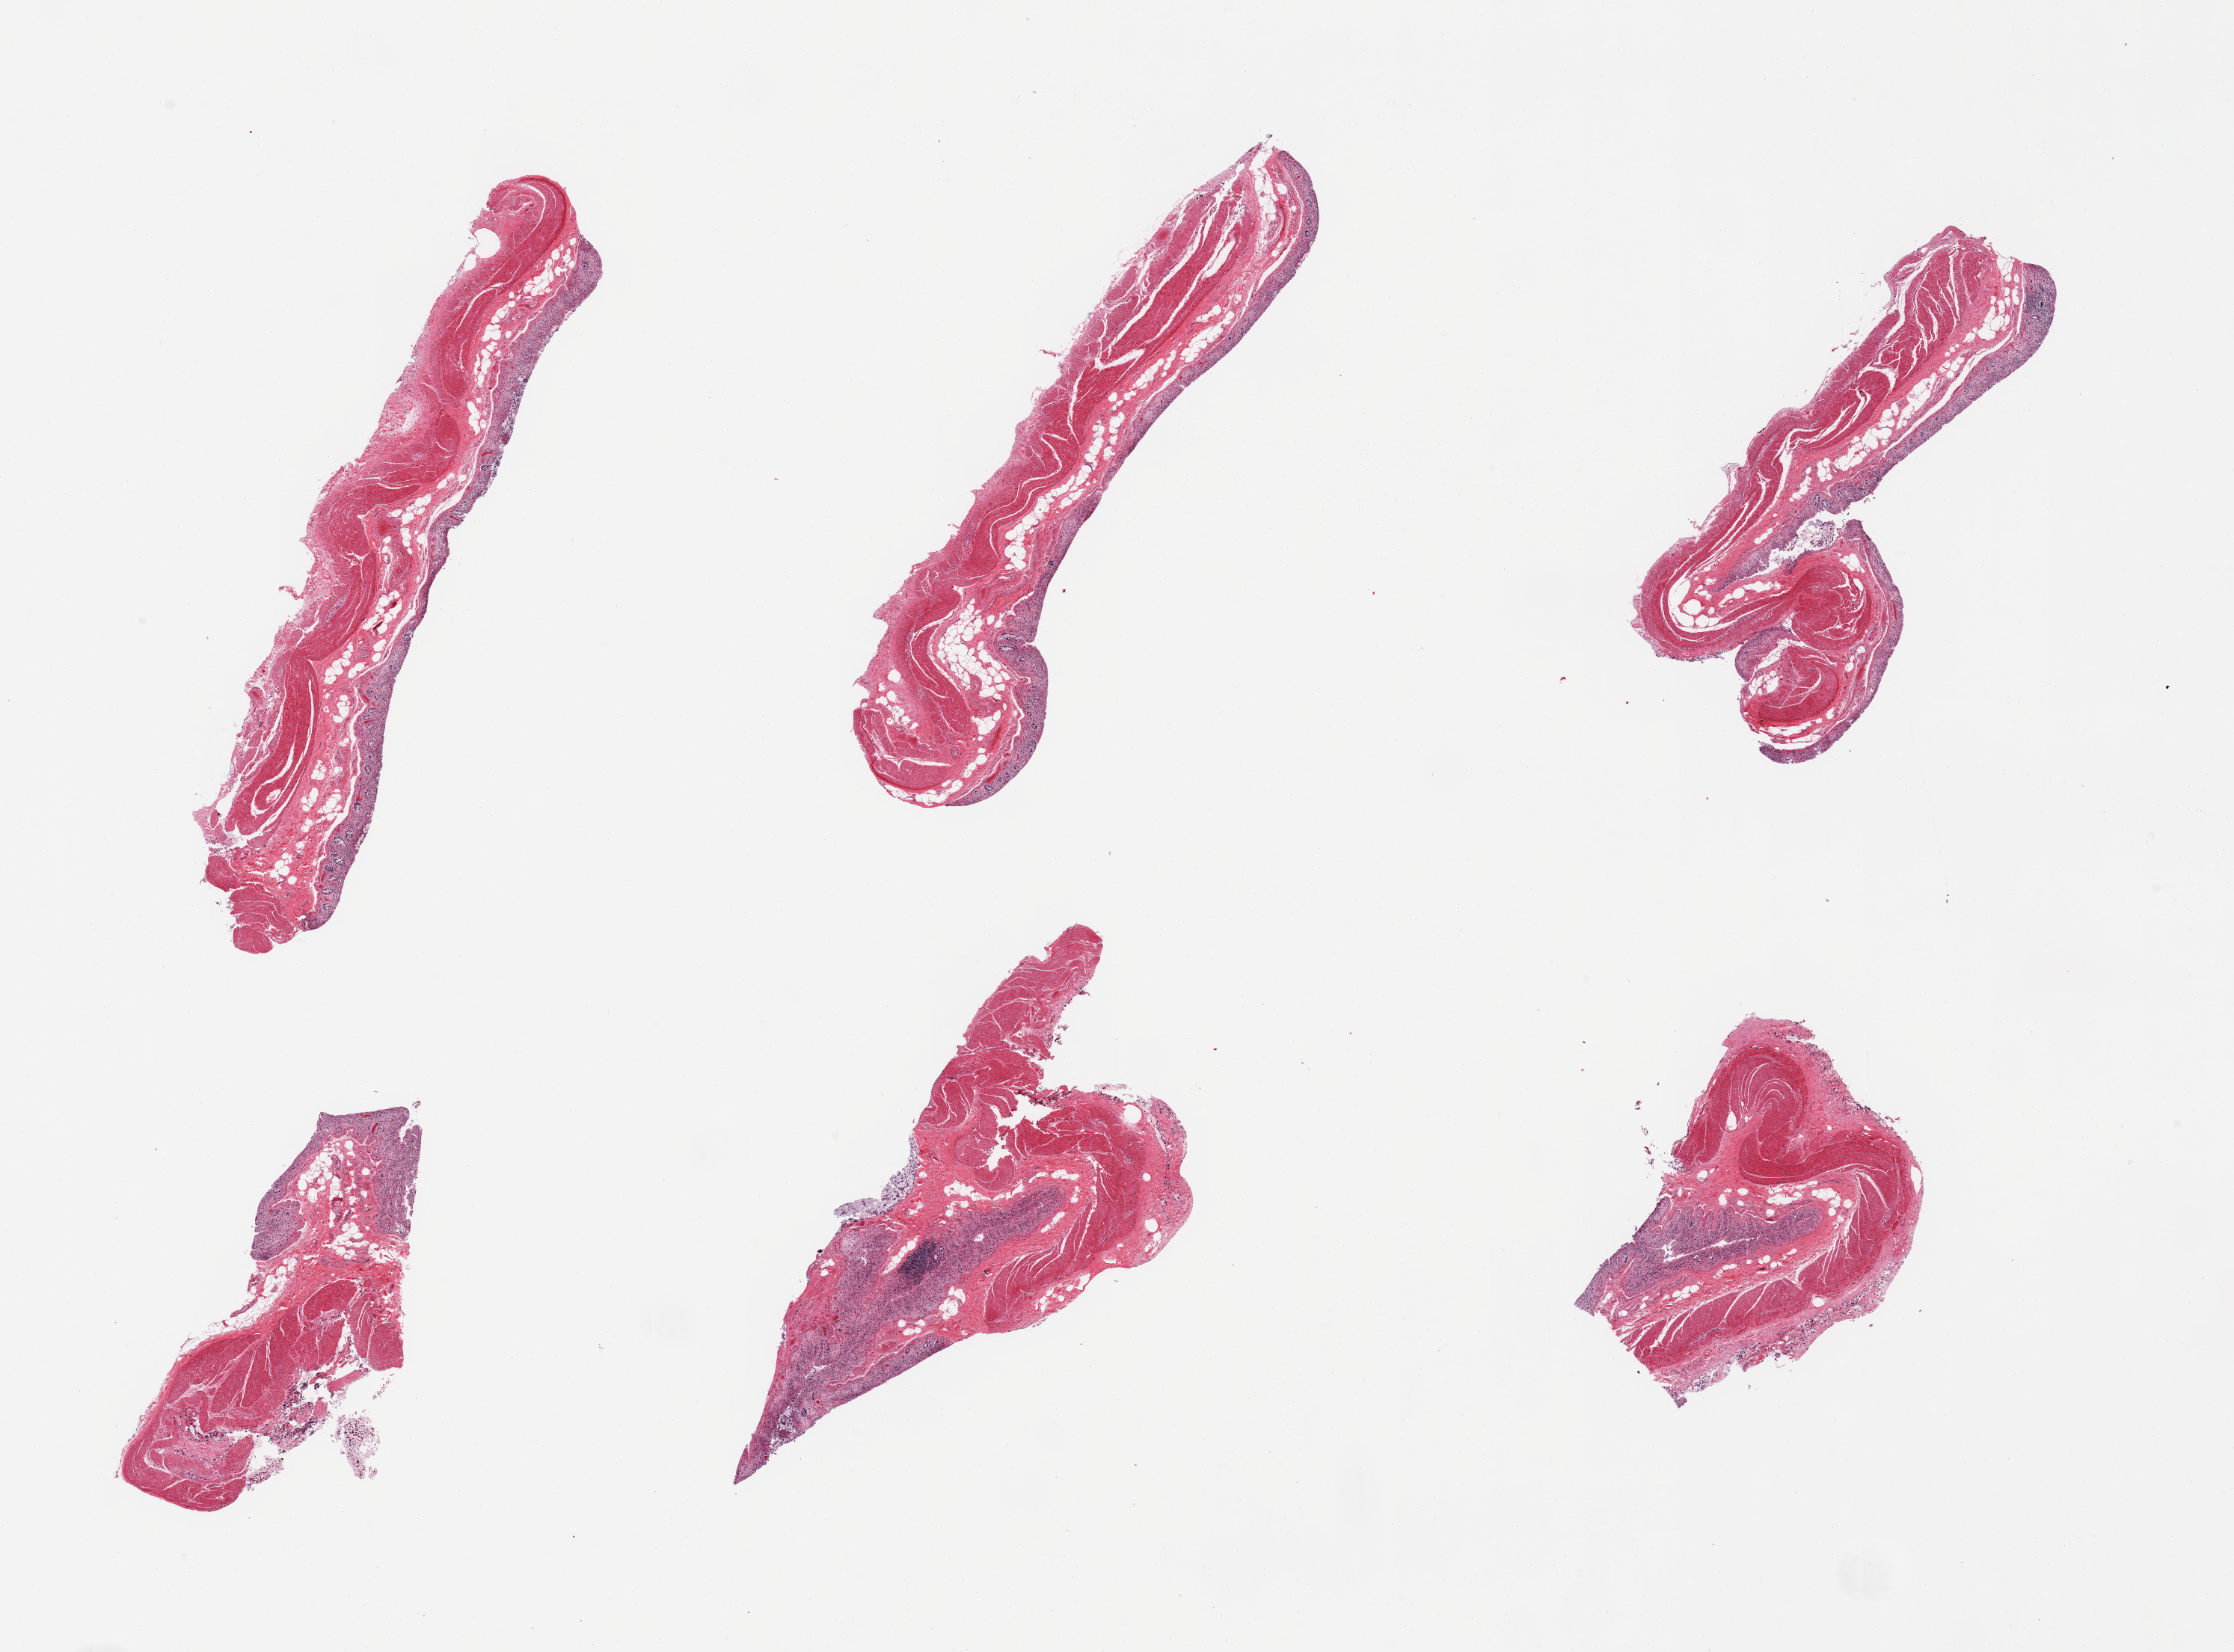
Haematoxylin and eosin whole-slide image, shown as a low-resolution overview of the whole scanned area (about 23.6 x 17.5 mm, acquisition: 20x scan); PAXgene-fixed, paraffin-embedded tissue; section of transverse colon (target tissue); donor tissue sample. Donor sex: male.
Review note (as recorded): 6 pieces, target mucosa with advanced glandular autolysis, up to ~0.3mm thick.